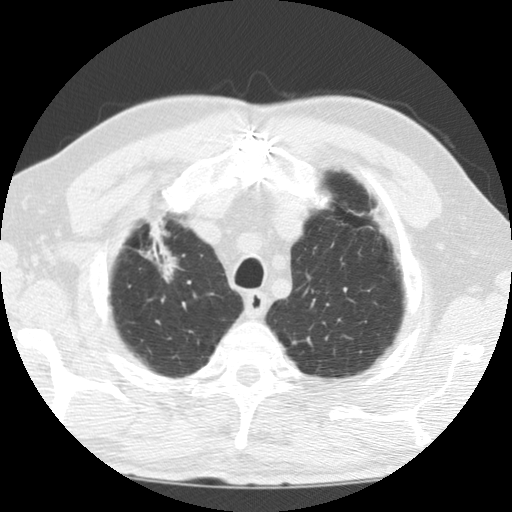
Chest CT (low-dose screening protocol), one axial image. Baseline annual screen. Lung window (W 1500 / L -600 HU). 512 × 512 image matrix, field of view 320 × 320 mm. Male, age 69 years at enrolment.
• Expert reader's lesion annotation, bounding box [x1, y1, x2, y2] px = [105, 214, 188, 294].
• Screening reader's record for this exam: no non-calcified nodule ≥4 mm recorded.
• Official screen result: negative screen, minor abnormalities not suspicious for lung cancer.
• Participant outcome: lung cancer diagnosed 171 days after this screen — adenocarcinoma, NOS, right upper lobe, poorly differentiated (G3), stage IIIB (AJCC 6th edition), 40 mm at pathology.